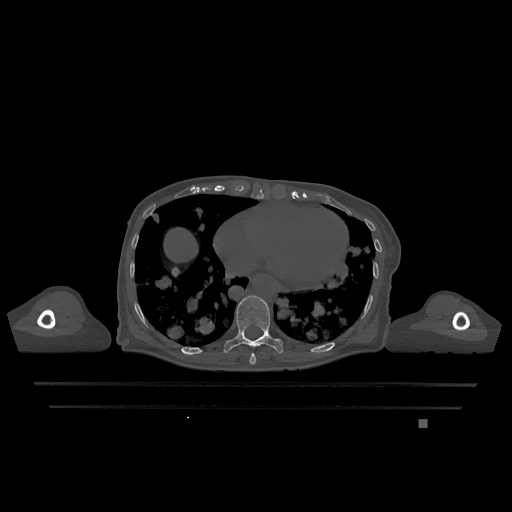
CT including the spine, one axial slice. Position 647 of 1317 along the scan axis. Bone window (W 1800 / L 400 HU). 0.5 mm slice thickness. 512 × 512 image matrix, field of view 500 × 500 mm. Female patient, age 74 years. Case-level facts recorded for this patient, not image findings: primary cancer: lung; vertebrae with lytic lesions (as recorded): T1, T4, T5, T6, L4, L5.
Structures marked on this image (semi-automatically segmented with operator editing):
- T10 vertebra: bounding box <223,295,284,353> (left, top, right, bottom; pixels)
- T9 vertebra: <249,353,256,365>